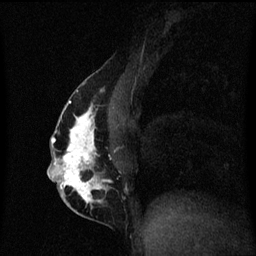
Breast MRI (dynamic contrast-enhanced), one sagittal slice; position 28 of 60 along the scan axis; dynamic contrast-enhanced series, image 2 of 3 at this slice position (ordered by acquisition); 1.5 T; TE 4.2 ms, TR 8.4 ms; 2 mm slice thickness; 256 × 256 image matrix. Female patient, age 40 years.
Outlined on this slice (semi-automatically segmented with operator editing):
- analysis volume of interest (the breast-tissue region the enhancement analysis was run in; not a lesion): bounding box [x1, y1, x2, y2] px = [49, 84, 120, 211]
- tumour enhancement mask (voxels above the 70 % enhancement threshold inside the analysis volume of interest): [49, 90, 107, 209]